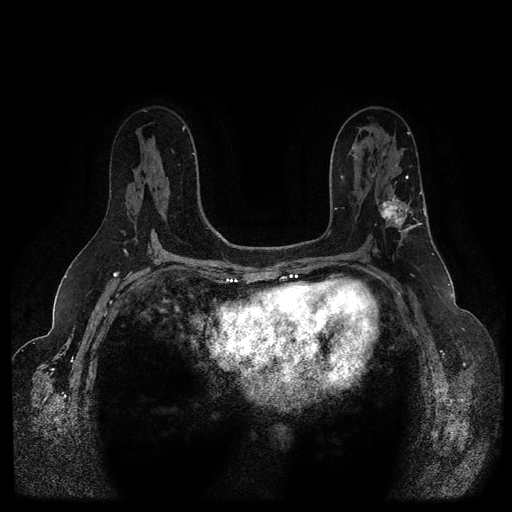
Breast MRI (dynamic contrast-enhanced, multi-phase), one axial slice; position 59 of 116 along the scan axis; dynamic contrast-enhanced series, time point 2 of 5 at this slice position (early post-contrast); 1.5 T; TE 2.6 ms, TR 5.3 ms; 2 mm slice thickness; 512 × 512 image matrix, field of view 350 × 350 mm. Female patient, age 54 years.
Annotated regions visible in this slice (semi-automatically segmented with operator editing):
- breast lesion (labelled 'tumour' in the annotation; benign lesions carry a separate 'benign' label): bounding box <377,193,410,229> (left, top, right, bottom; pixels)